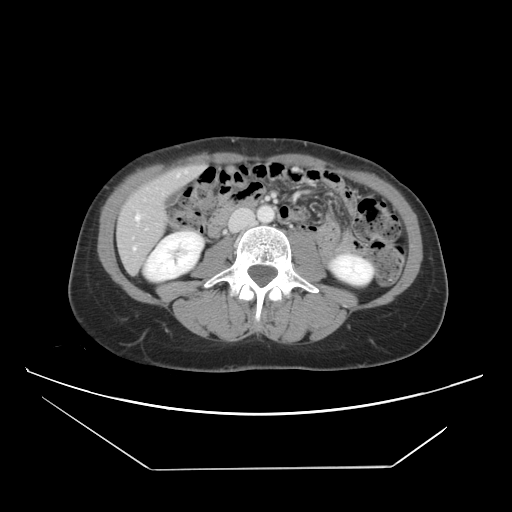
Contrast-enhanced abdominal CT, one axial slice; 120 kVp; intravenous contrast given; soft-tissue window (W 400 / L 40 HU); 5 mm slice thickness; 512 × 512 image matrix, field of view 399 × 399 mm. Female patient, age 52 years. Case-level facts recorded for this patient, not image findings: diagnosis: colorectal cancer liver metastases, imaged before liver resection; multiple liver metastases: yes; largest metastasis: 5.5 cm.
Outlined on this slice (manually delineated by an expert):
- hepatic veins: bounding box <134,168,202,250> (left, top, right, bottom; pixels)
- liver: <118,168,198,271>
- planned liver remnant (the part of the liver to remain after resection): <126,168,197,217>
- portal vein (with intrahepatic branches): <266,197,270,200>